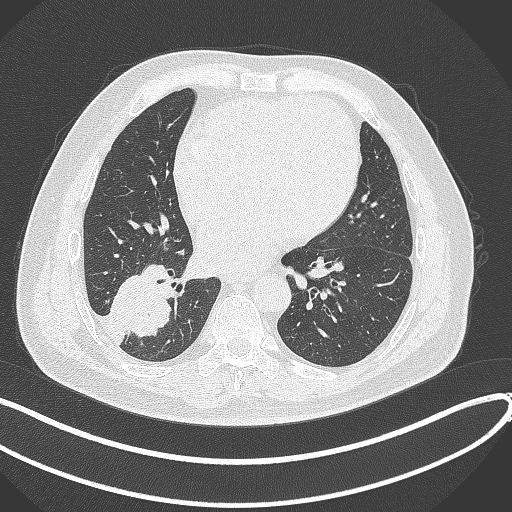
Chest CT, one axial slice. Slice 145 of 360 in the series (ordered by position). 120 kVp. Lung window (W 1500 / L -600 HU). 512 × 512 image matrix. Male patient, age 59 years.
Outlined on this slice (rectangle marked by the reading radiologist):
- lung tumour (recorded histology: adenocarcinoma): bounding box (x1, y1, x2, y2) in pixels: (107, 257, 176, 338)